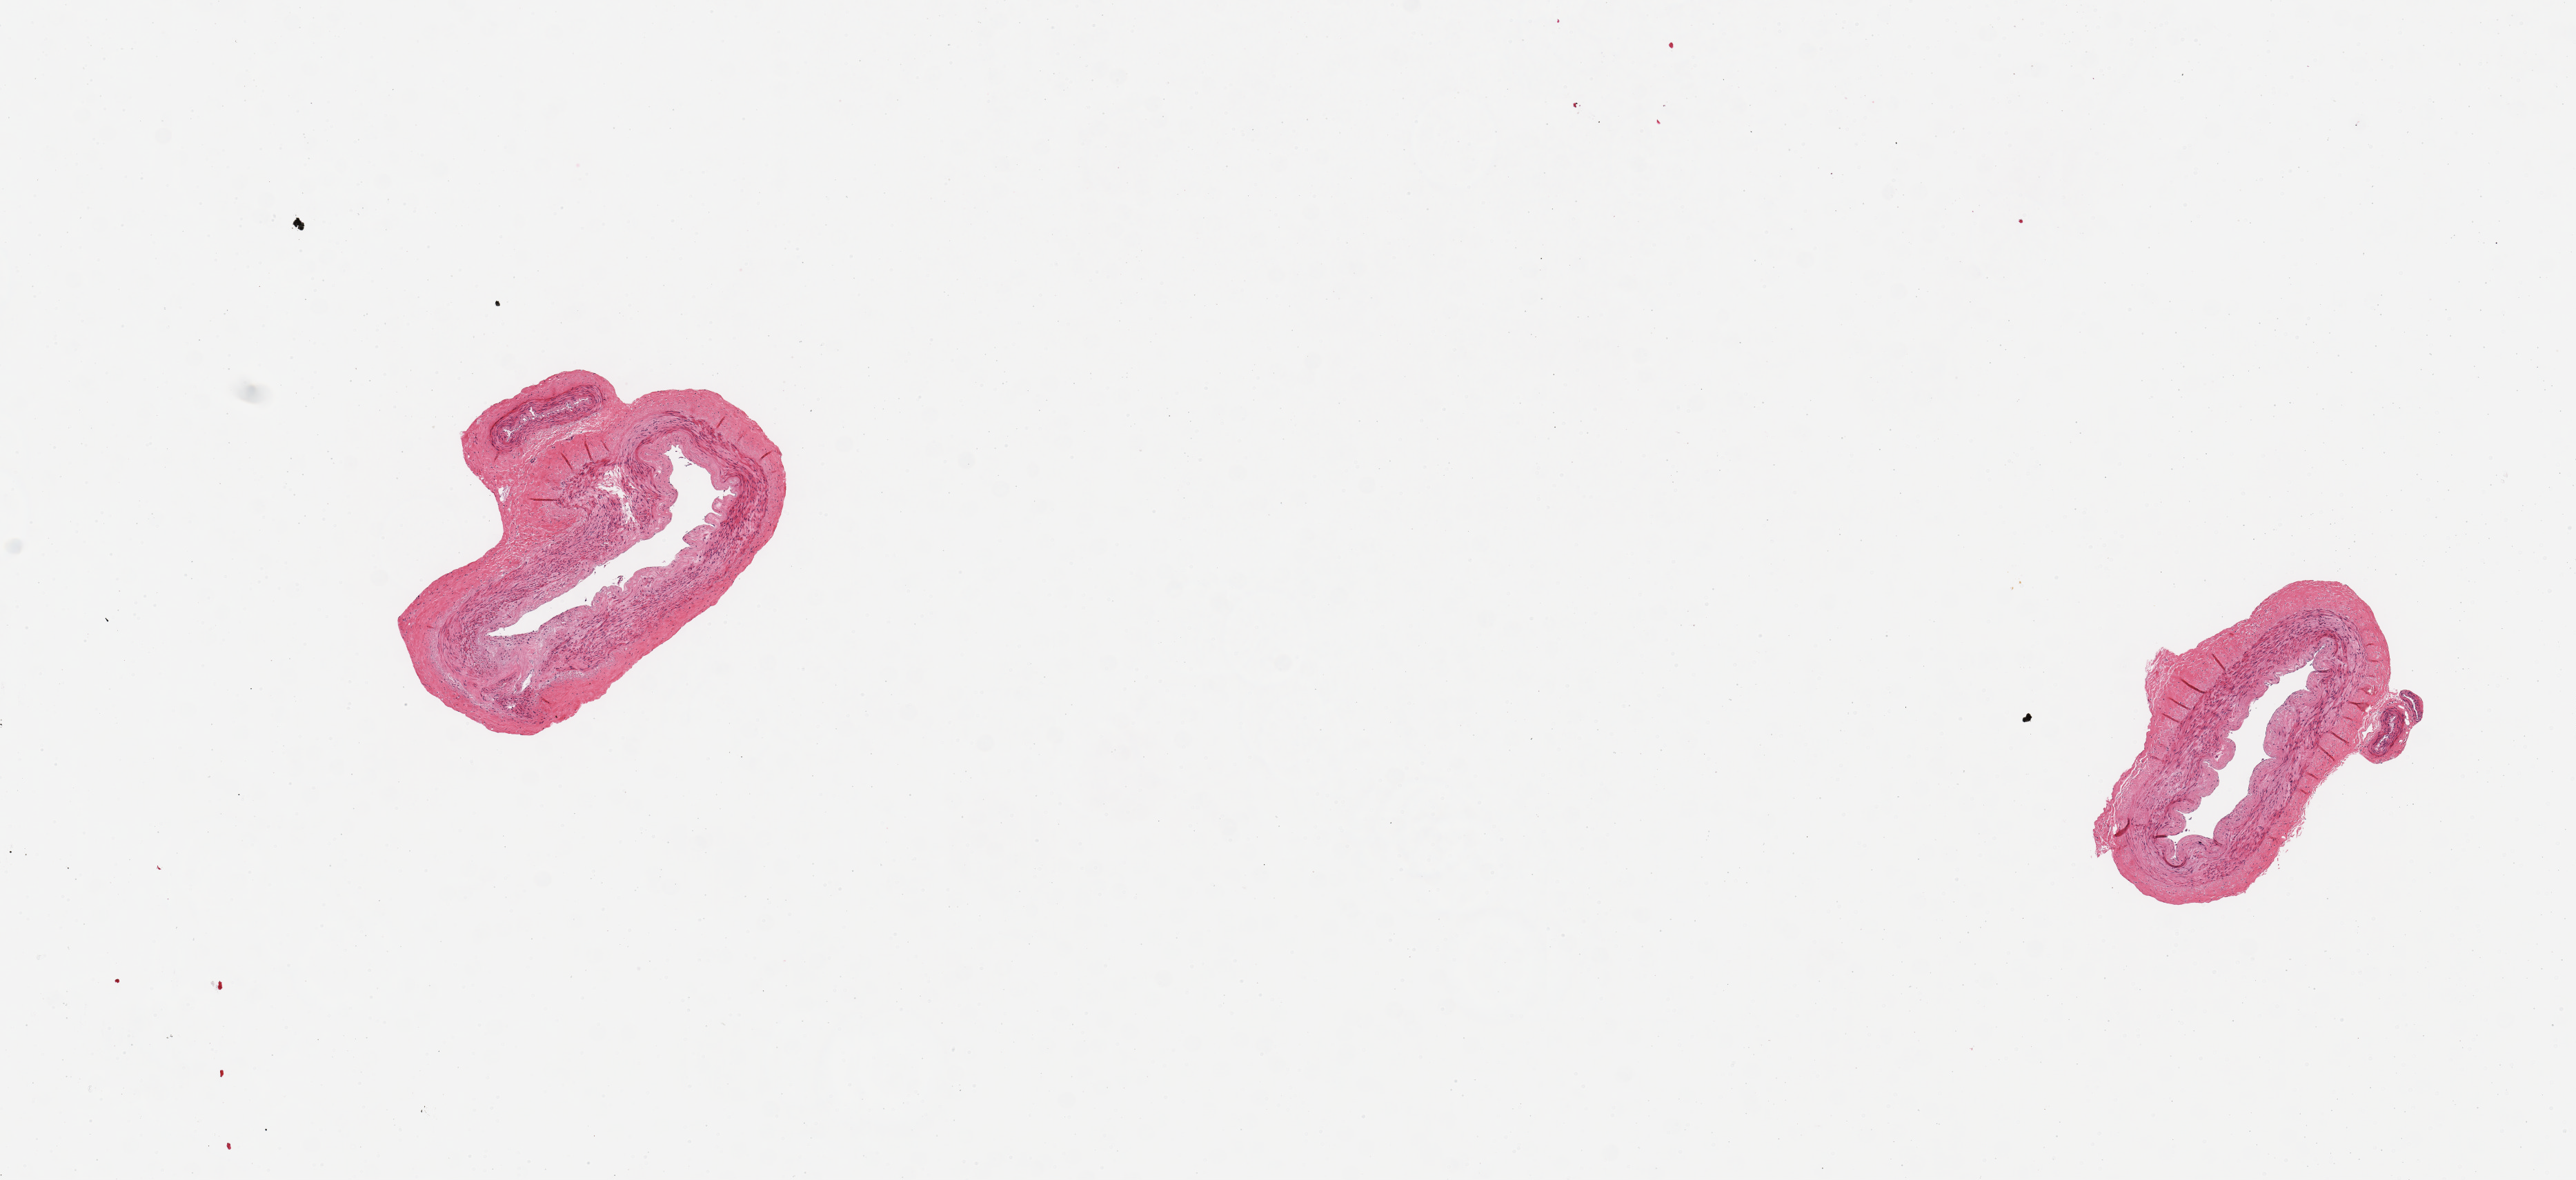
Whole-slide image, haematoxylin and eosin stain — a low-resolution overview of the entire scanned area, about 14.8 x 6.8 mm; PAXgene-fixed, paraffin-embedded tissue; section of tibial artery (target tissue); donor tissue sample. Donor sex: female.
Pathologist's review note for this sample: 2 pieces, no adherent fat, excellent specimens. One section near bifurcation of smaller vessel.